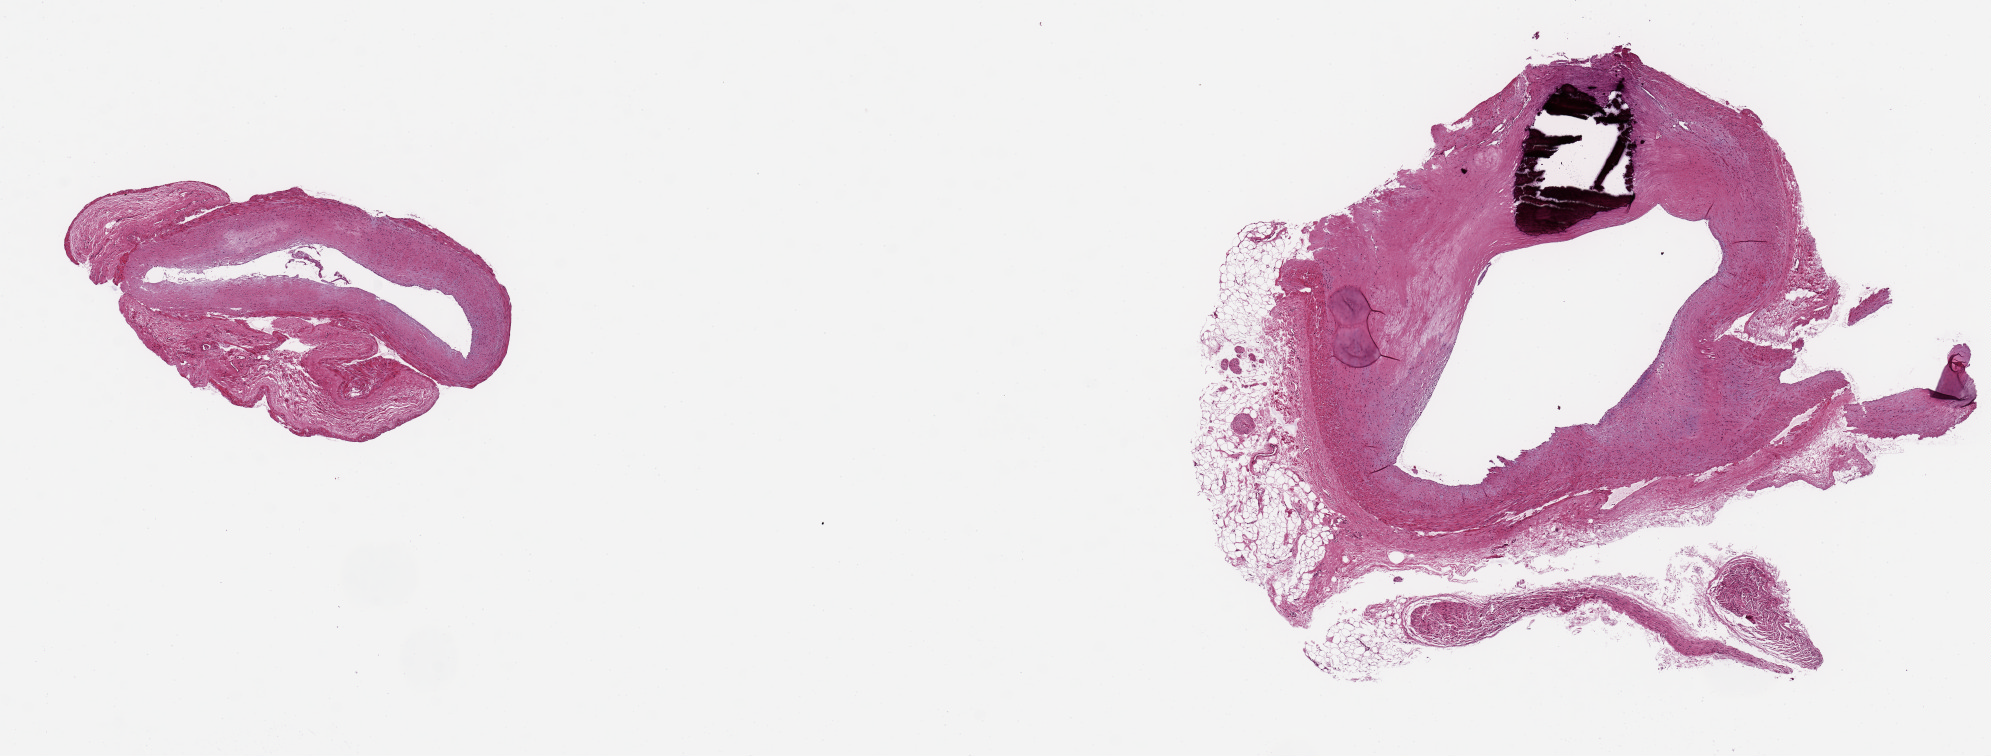
Haematoxylin and eosin whole-slide image, shown as a low-resolution overview of the whole scanned area (about 15.8 x 6.0 mm, acquisition: 20x scan), PAXgene-fixed paraffin-embedded (PFPE) section, sampled site (target tissue): coronary artery, donor tissue sample.
Review note (as recorded): 2 pieces 5x4 & 3x2 mm; larger with focally calcified plaque & 50% occlusion & 10% adipose.